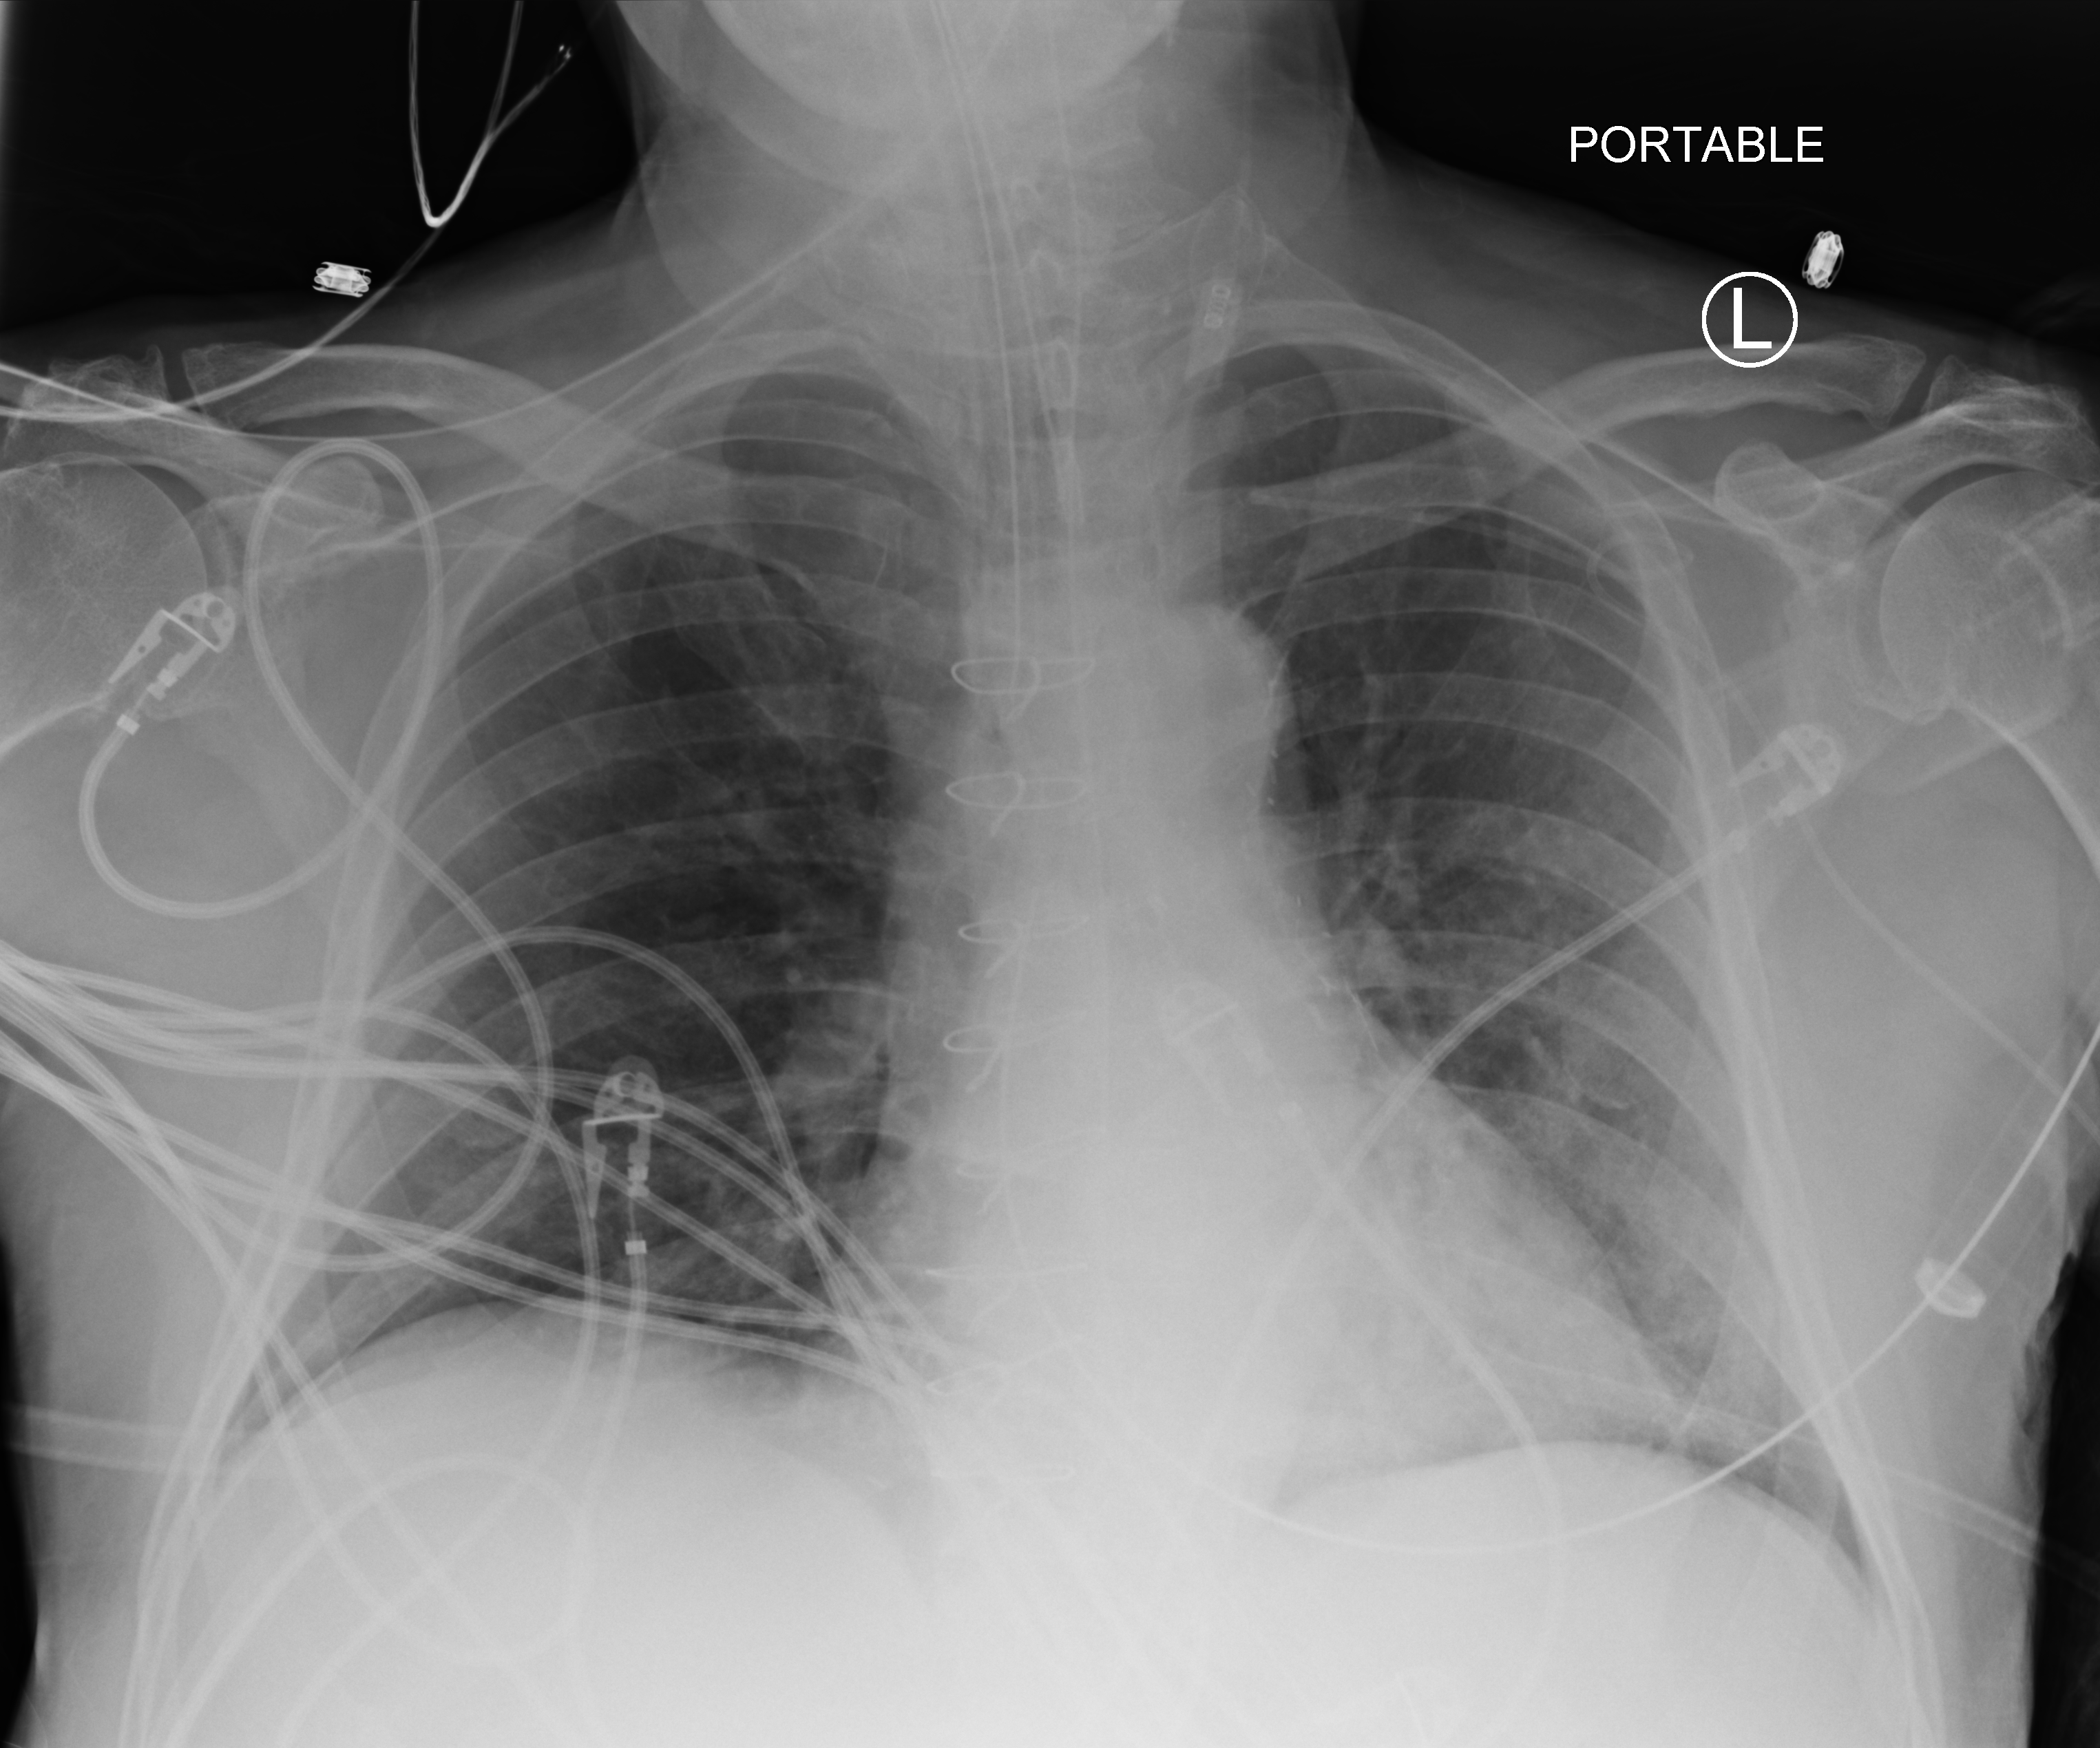
Bedside chest radiograph (computed radiography); anteroposterior (AP) projection. Male patient hospitalised with COVID-19, age 60–74 years.
Hospital-stay facts (about this admission, not read from this image; timing relative to this image not recorded):
- mechanically ventilated during this hospital stay: yes
- hypertension (admission record): yes